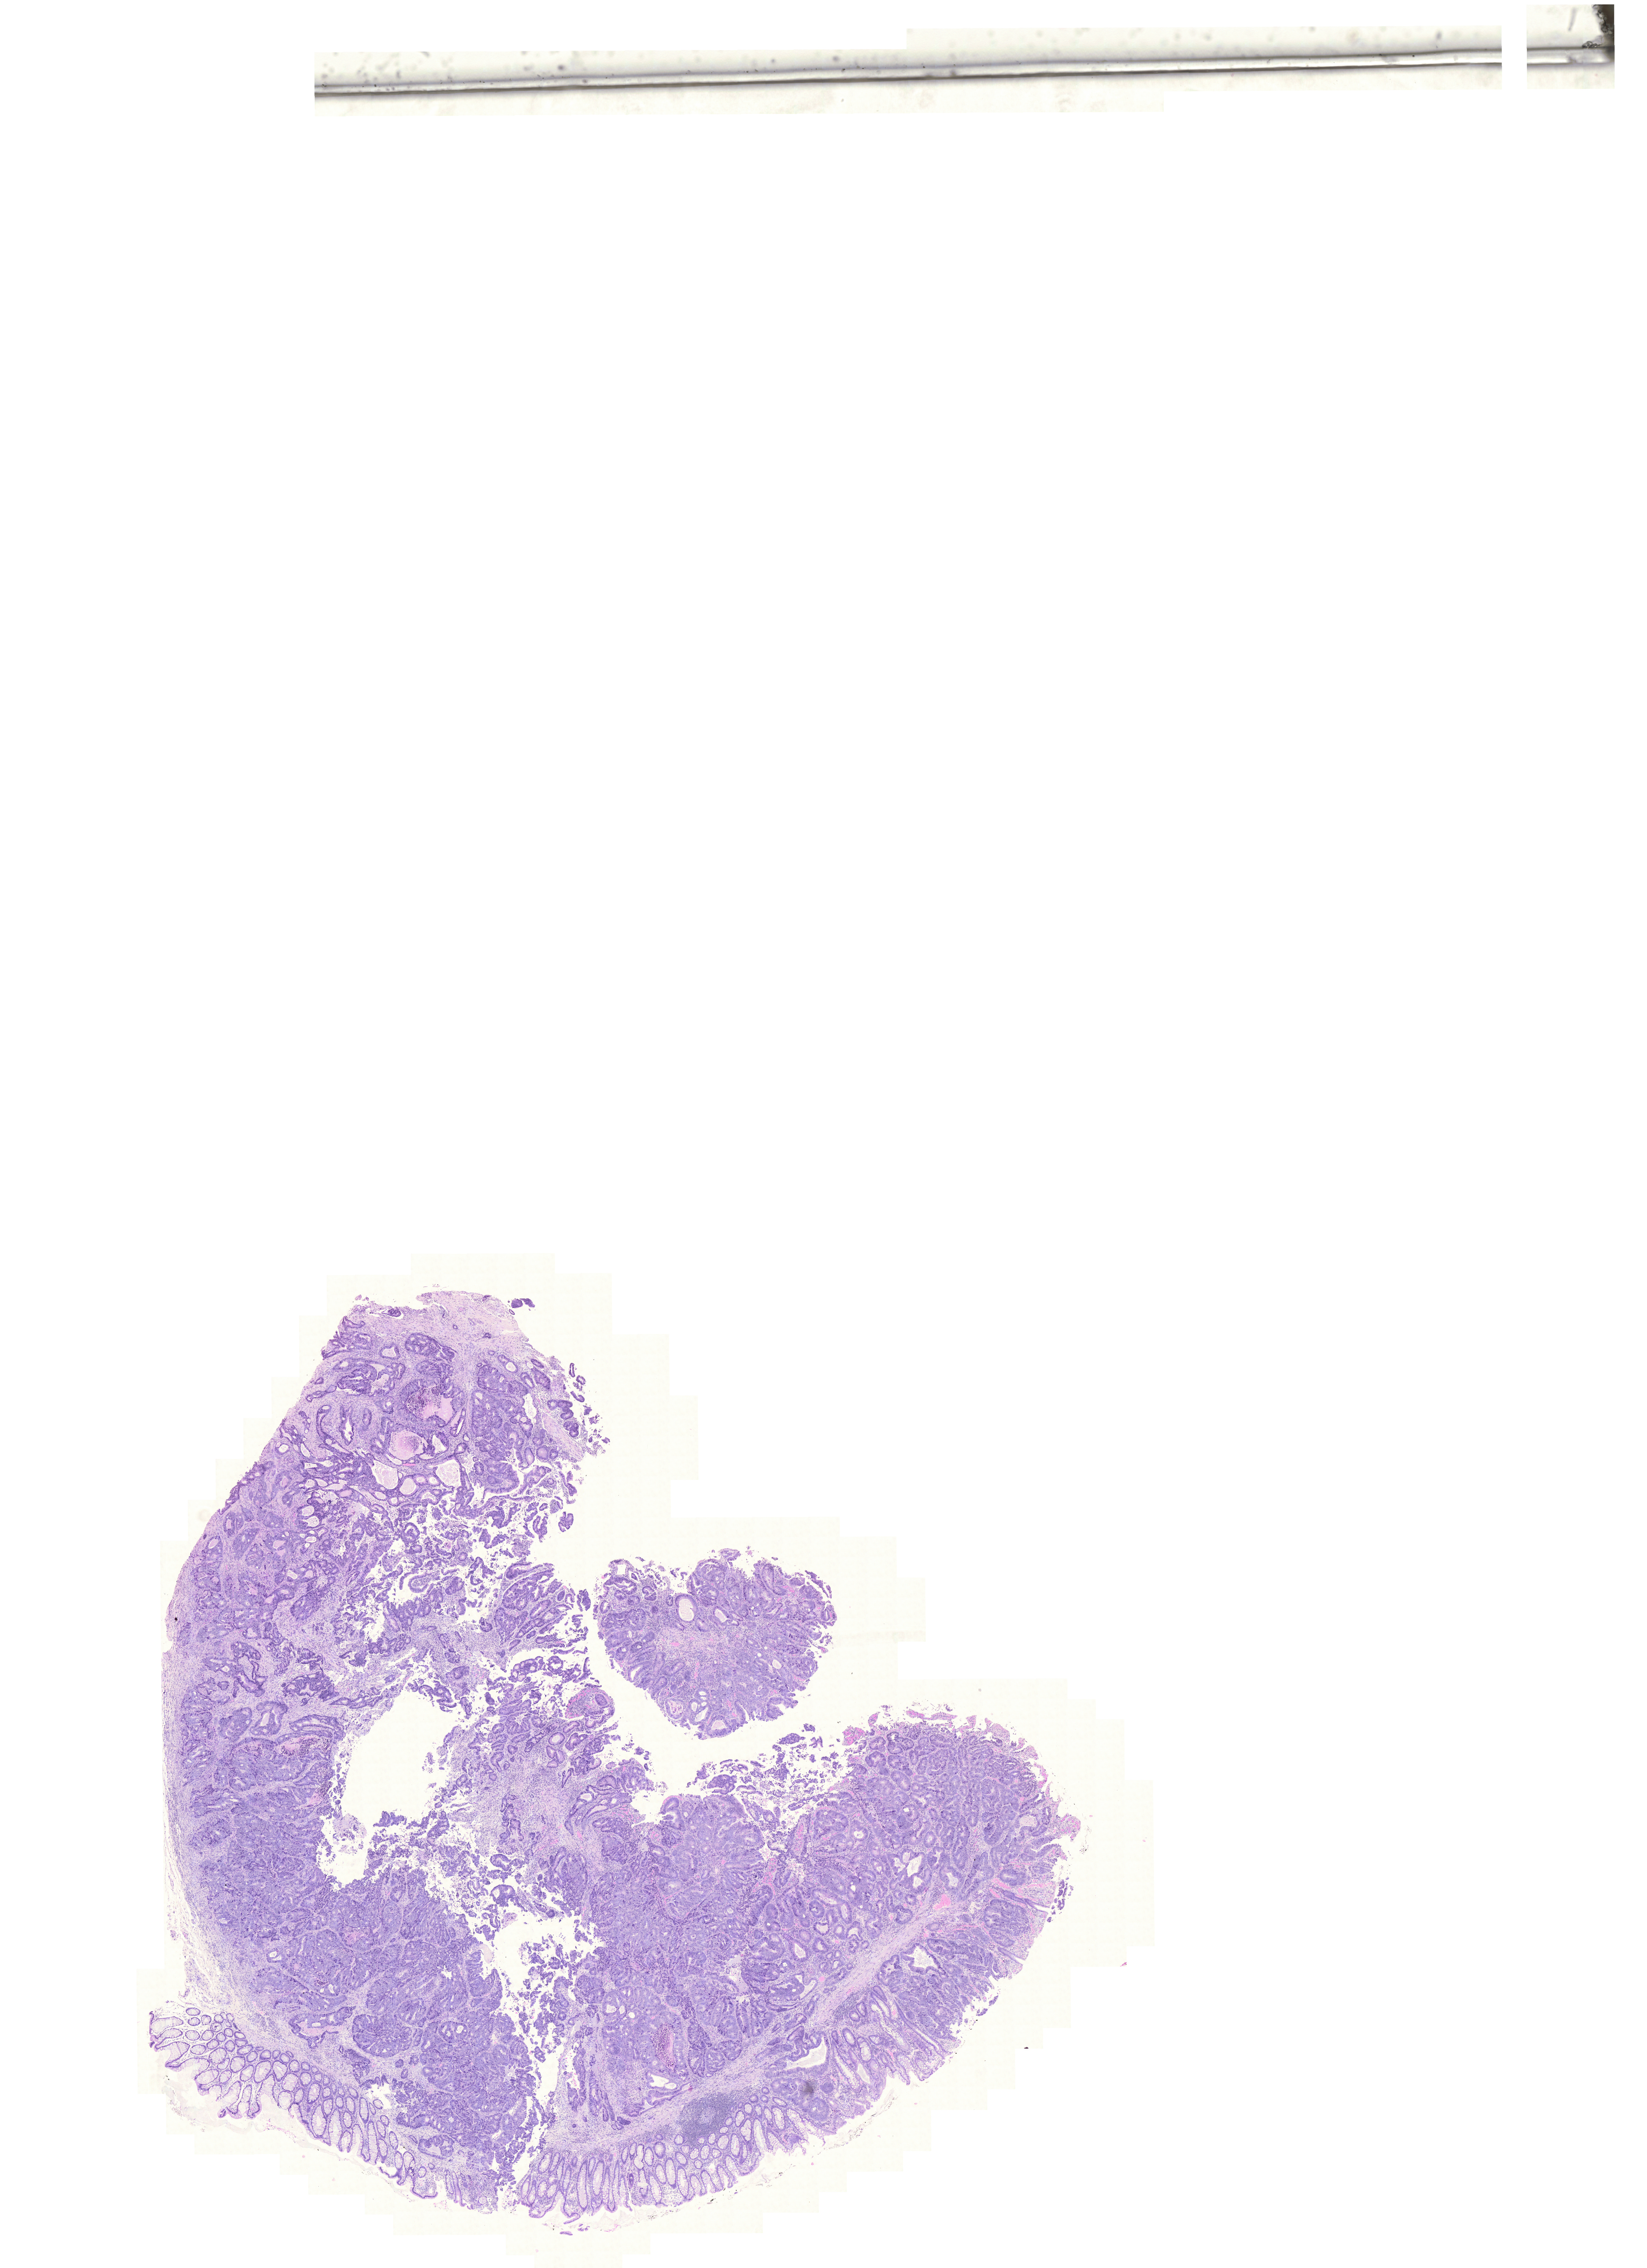
Digitized H&E tissue section (whole slide), shown as a low-resolution overview of the whole scanned area (about 16.7 x 23.0 mm, acquisition: 20x scan). Formalin-fixed paraffin-embedded (FFPE) diagnostic section. Primary tumour sample from the colon. Female, age 74 years at initial diagnosis.
Diagnosis: Adenocarcinoma, NOS.